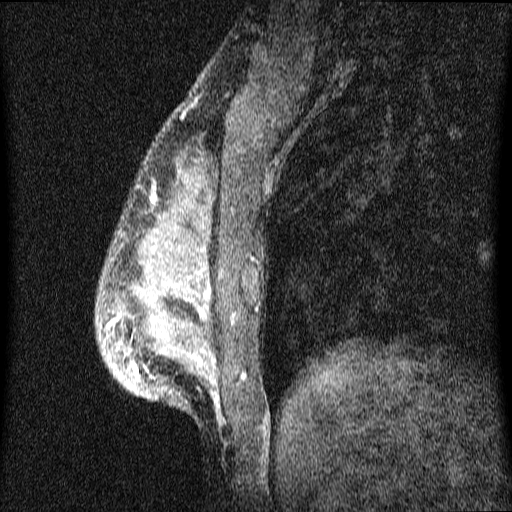
Breast MRI (dynamic contrast-enhanced), one sagittal slice; position 18 of 64 along the scan axis; dynamic contrast-enhanced series, image 2 of 4 at this slice position (ordered by acquisition); 1.5 T; TE 4.2 ms, TR 9.1 ms; 2 mm slice thickness; 512 × 512 image matrix, field of view 180 × 180 mm. Patient: female, 33 years.
Structures marked on this image (semi-automatically segmented with operator editing):
- analysis volume of interest (the breast-tissue region the enhancement analysis was run in; not a lesion): bounding box <96,151,309,450> (left, top, right, bottom; pixels)
- tumour enhancement mask (voxels above the 70 % enhancement threshold inside the analysis volume of interest): <109,189,218,403>